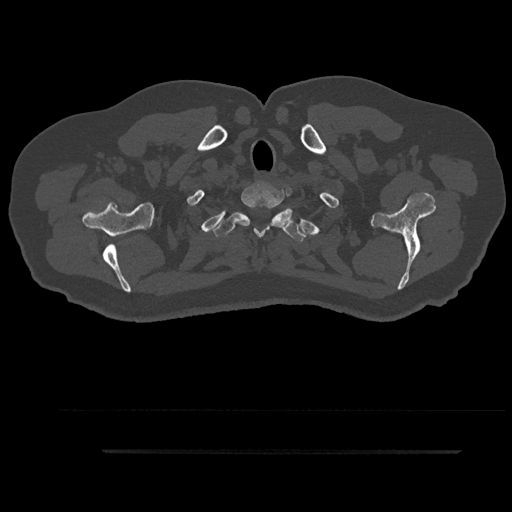
CT including the spine, one axial slice. Position 781 of 797 along the scan axis. Reconstruction kernel Br40s/3. 120 kVp. Bone window (W 1800 / L 400 HU). 512 × 512 image matrix, field of view 432 × 432 mm. Male patient, age 63 years. From the clinical record (not read from this slice): primary cancer: renal; vertebrae with lytic lesions (as recorded): T8.
Structures marked on this image (semi-automatic segmentation, software-assisted and operator-edited):
- T1 vertebra: bounding box [x1, y1, x2, y2] px = [232, 185, 291, 236]
- T2 vertebra: [213, 206, 306, 242]